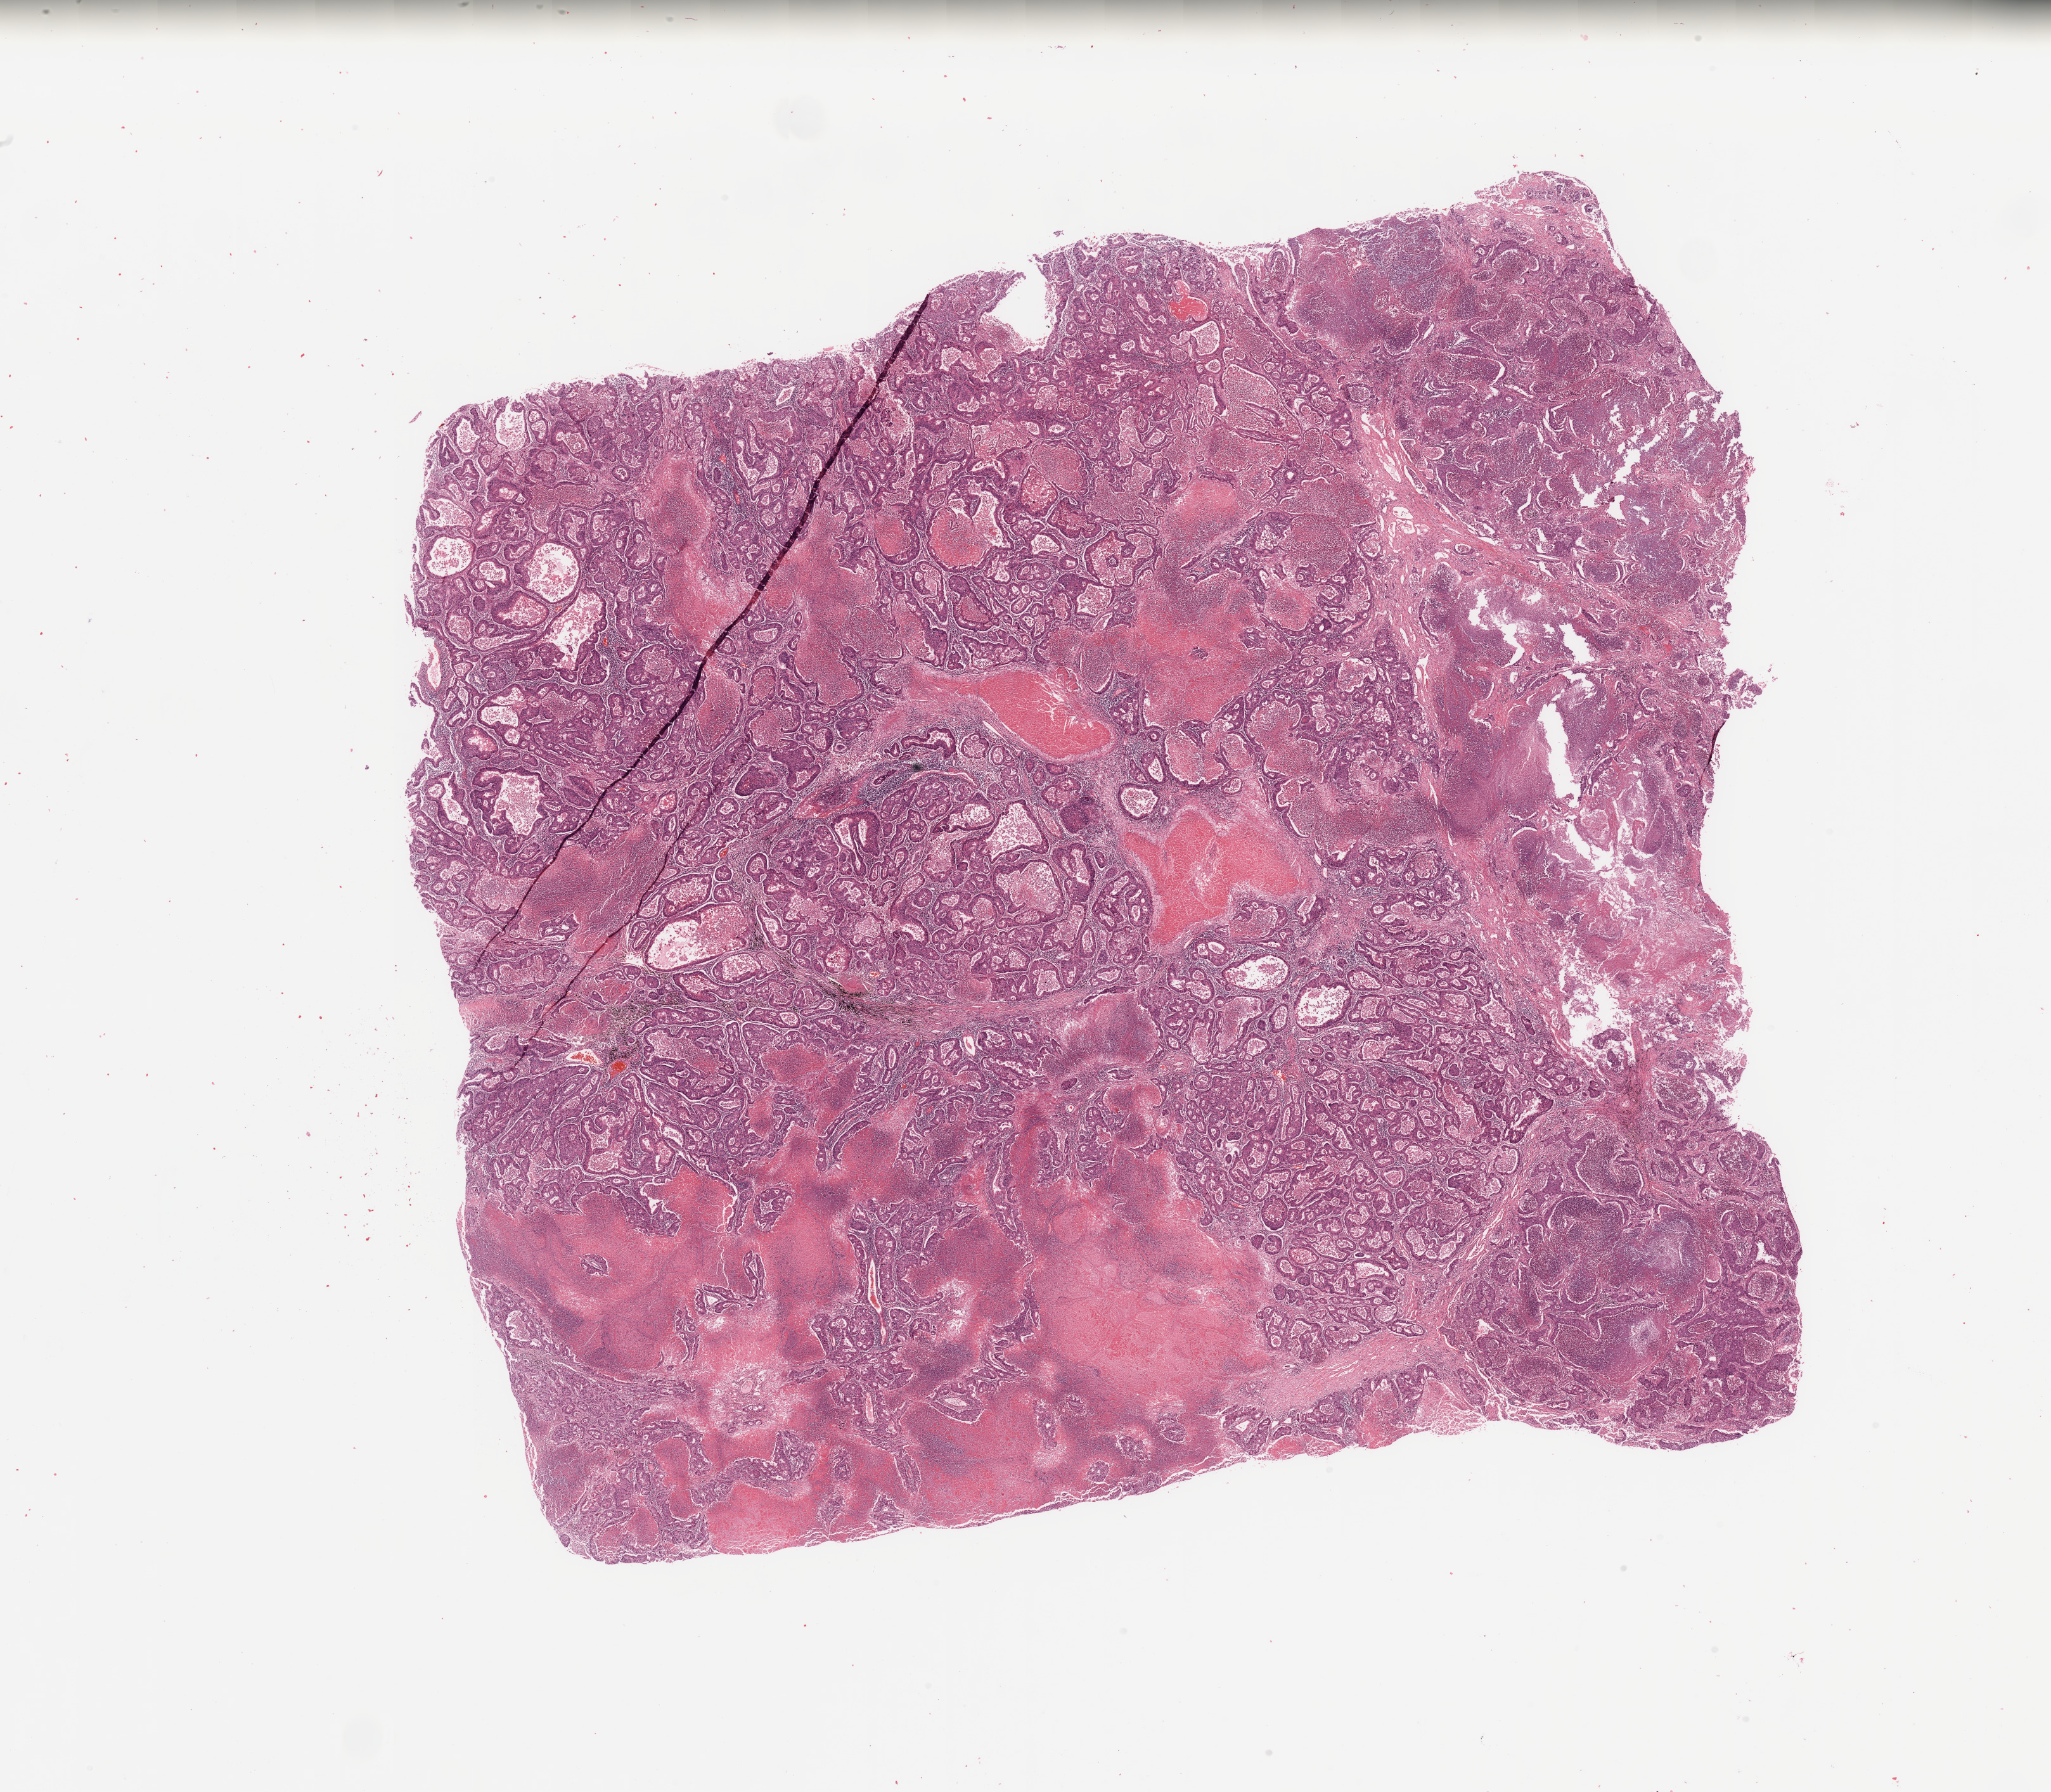
Whole-slide histology image, H&E — shown as a low-resolution overview of the whole scanned area (about 25.6 x 22.4 mm, from a 20x scan); tumour tissue sample, sampled site: lung. Male, 76 y/o.
Diagnosis: Adenocarcinoma, NOS.